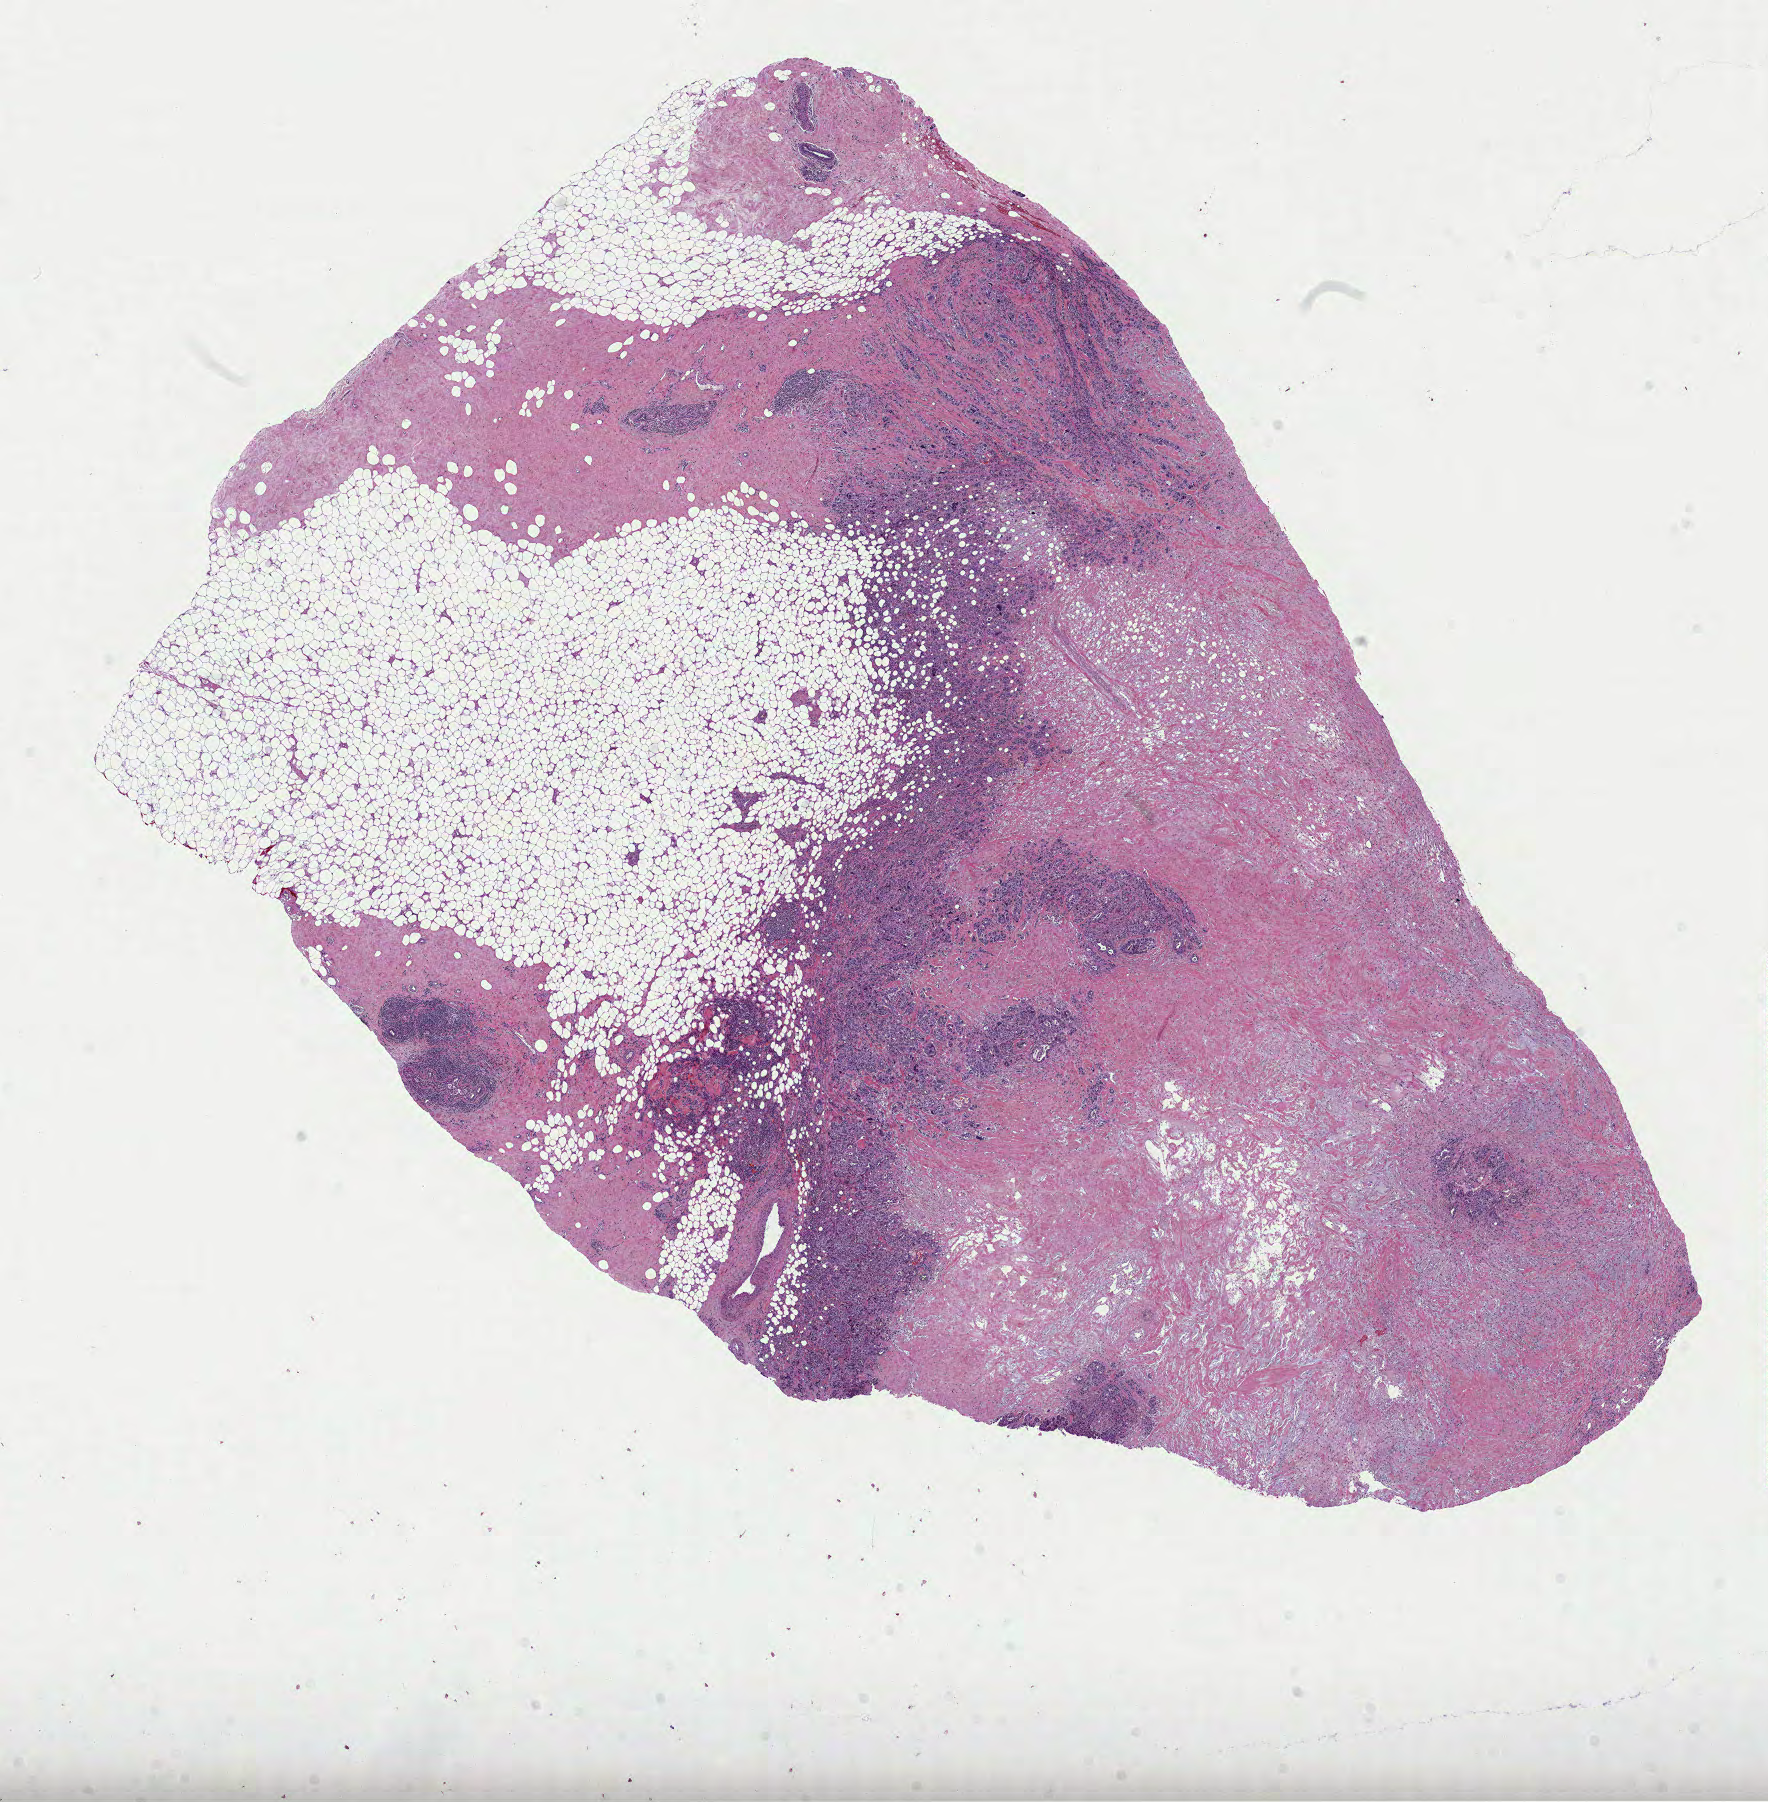
Digitized H&E tissue section (whole slide) — shown as a low-resolution overview of the whole scanned area (about 14.3 x 14.5 mm). Formalin-fixed paraffin-embedded (FFPE) diagnostic section. Primary tumour sample from the breast. Female, age 72 years at initial diagnosis.
Histologic diagnosis: Infiltrating duct carcinoma, NOS. AJCC pathologic stage: IIB (7th edition). TNM: T2 N1a MX. Lymph nodes positive (case pathology): 1 of 2 examined.